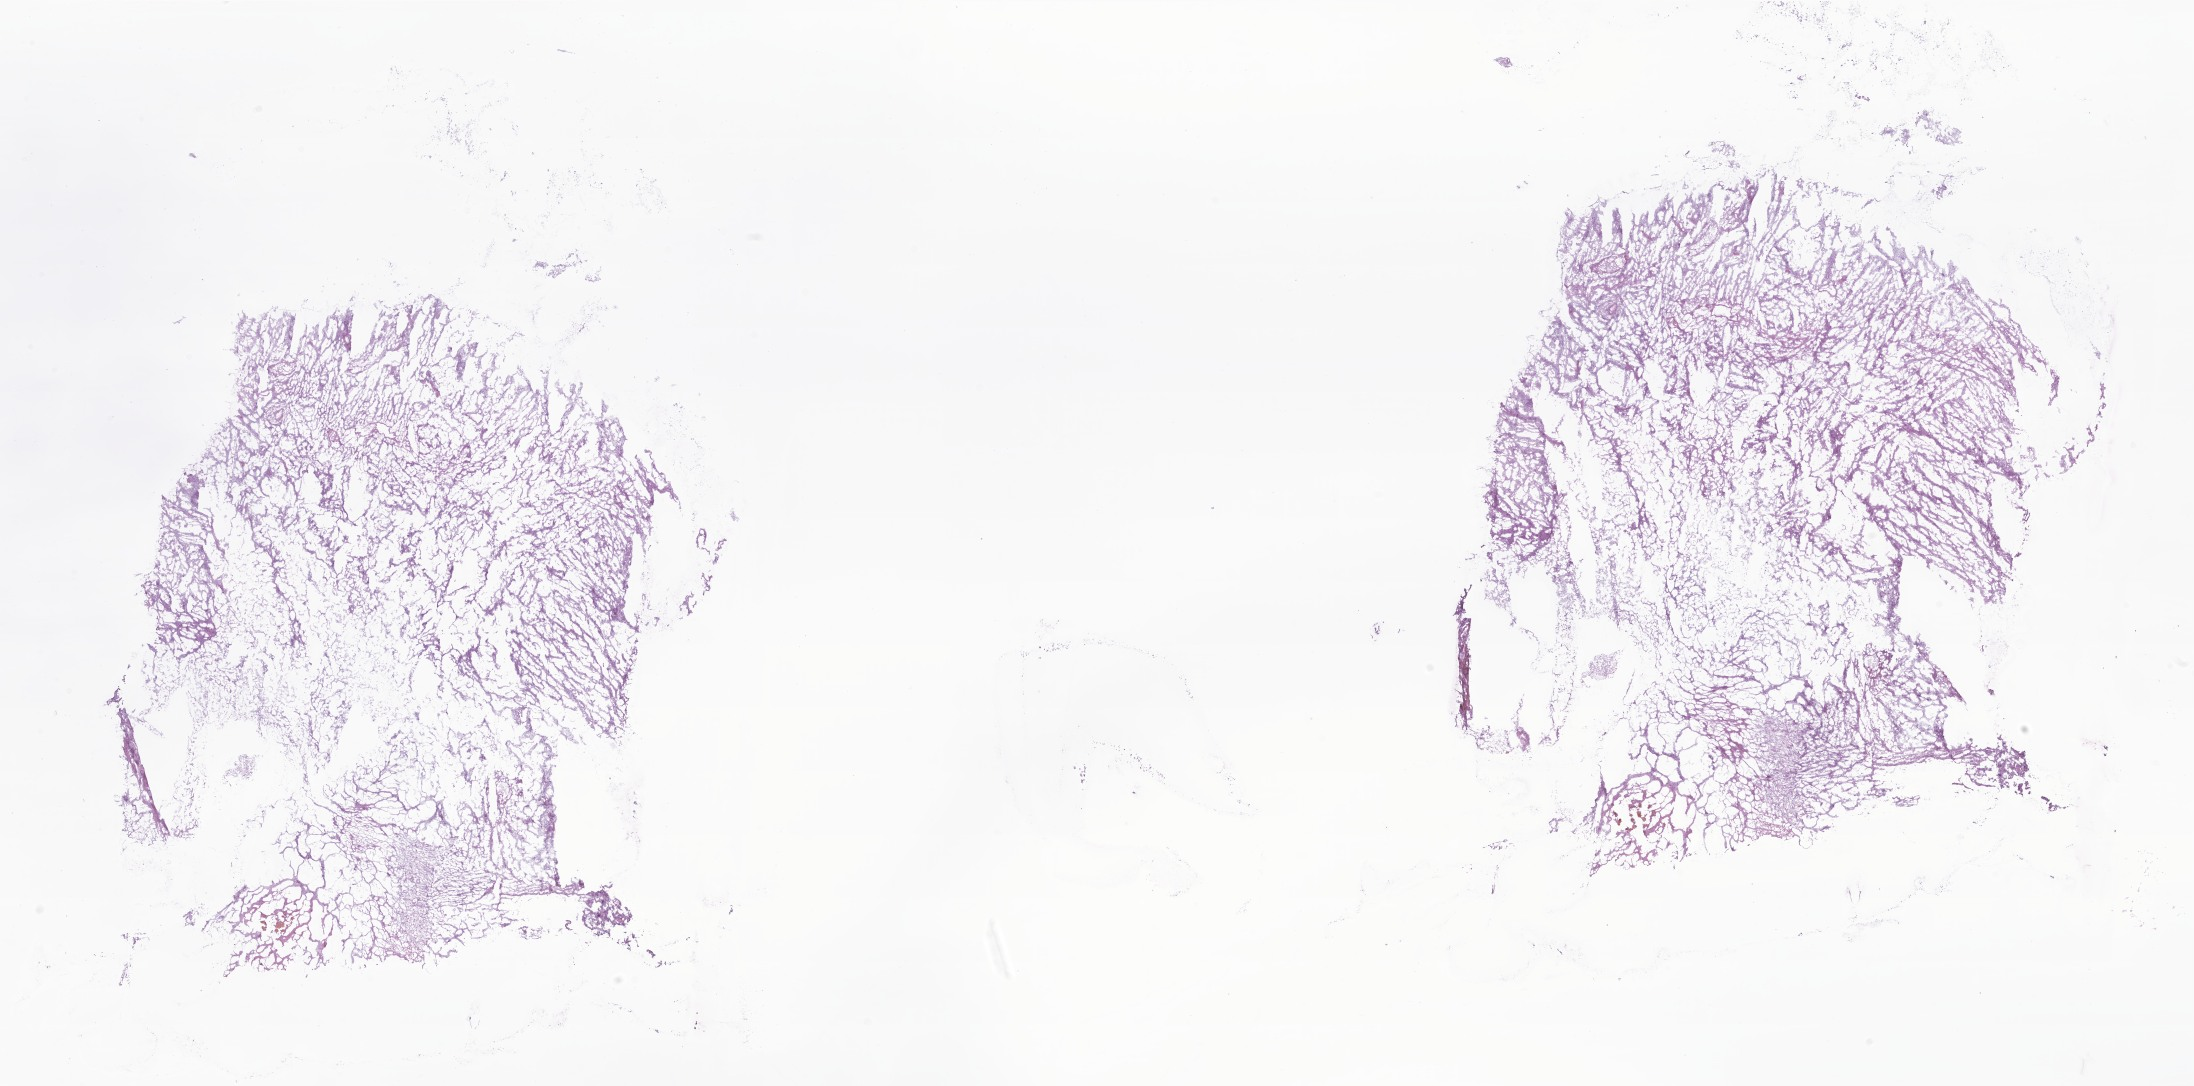
Whole-slide image, H&E stain of tumor tissue from the cerebral ventricle — low-resolution overview of the scanned area, about 37.0 x 18.3 mm, frozen section (OCT-embedded). Patient male; age 36 months (3 years).
Recorded diagnosis: Astrocytoma, NOS.